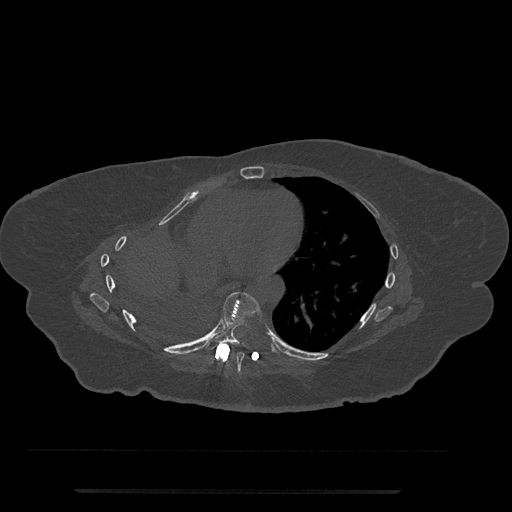
CT including the spine, one axial slice; slice 407 of 797 in the series (ordered by position); 120 kVp; bone window (W 1800 / L 400 HU); 0.5 mm slice thickness; 512 × 512 image matrix, field of view 440 × 440 mm. Female patient, age 51 years. Case-level facts recorded for this patient, not image findings: primary cancer: neuro; vertebrae with lytic lesions (as recorded): T8.
Structures marked on this image (semi-automatically segmented with operator editing):
- T7 vertebra: bounding box (x1, y1, x2, y2) in pixels: (231, 352, 245, 374)
- T8 vertebra: (205, 292, 261, 352)